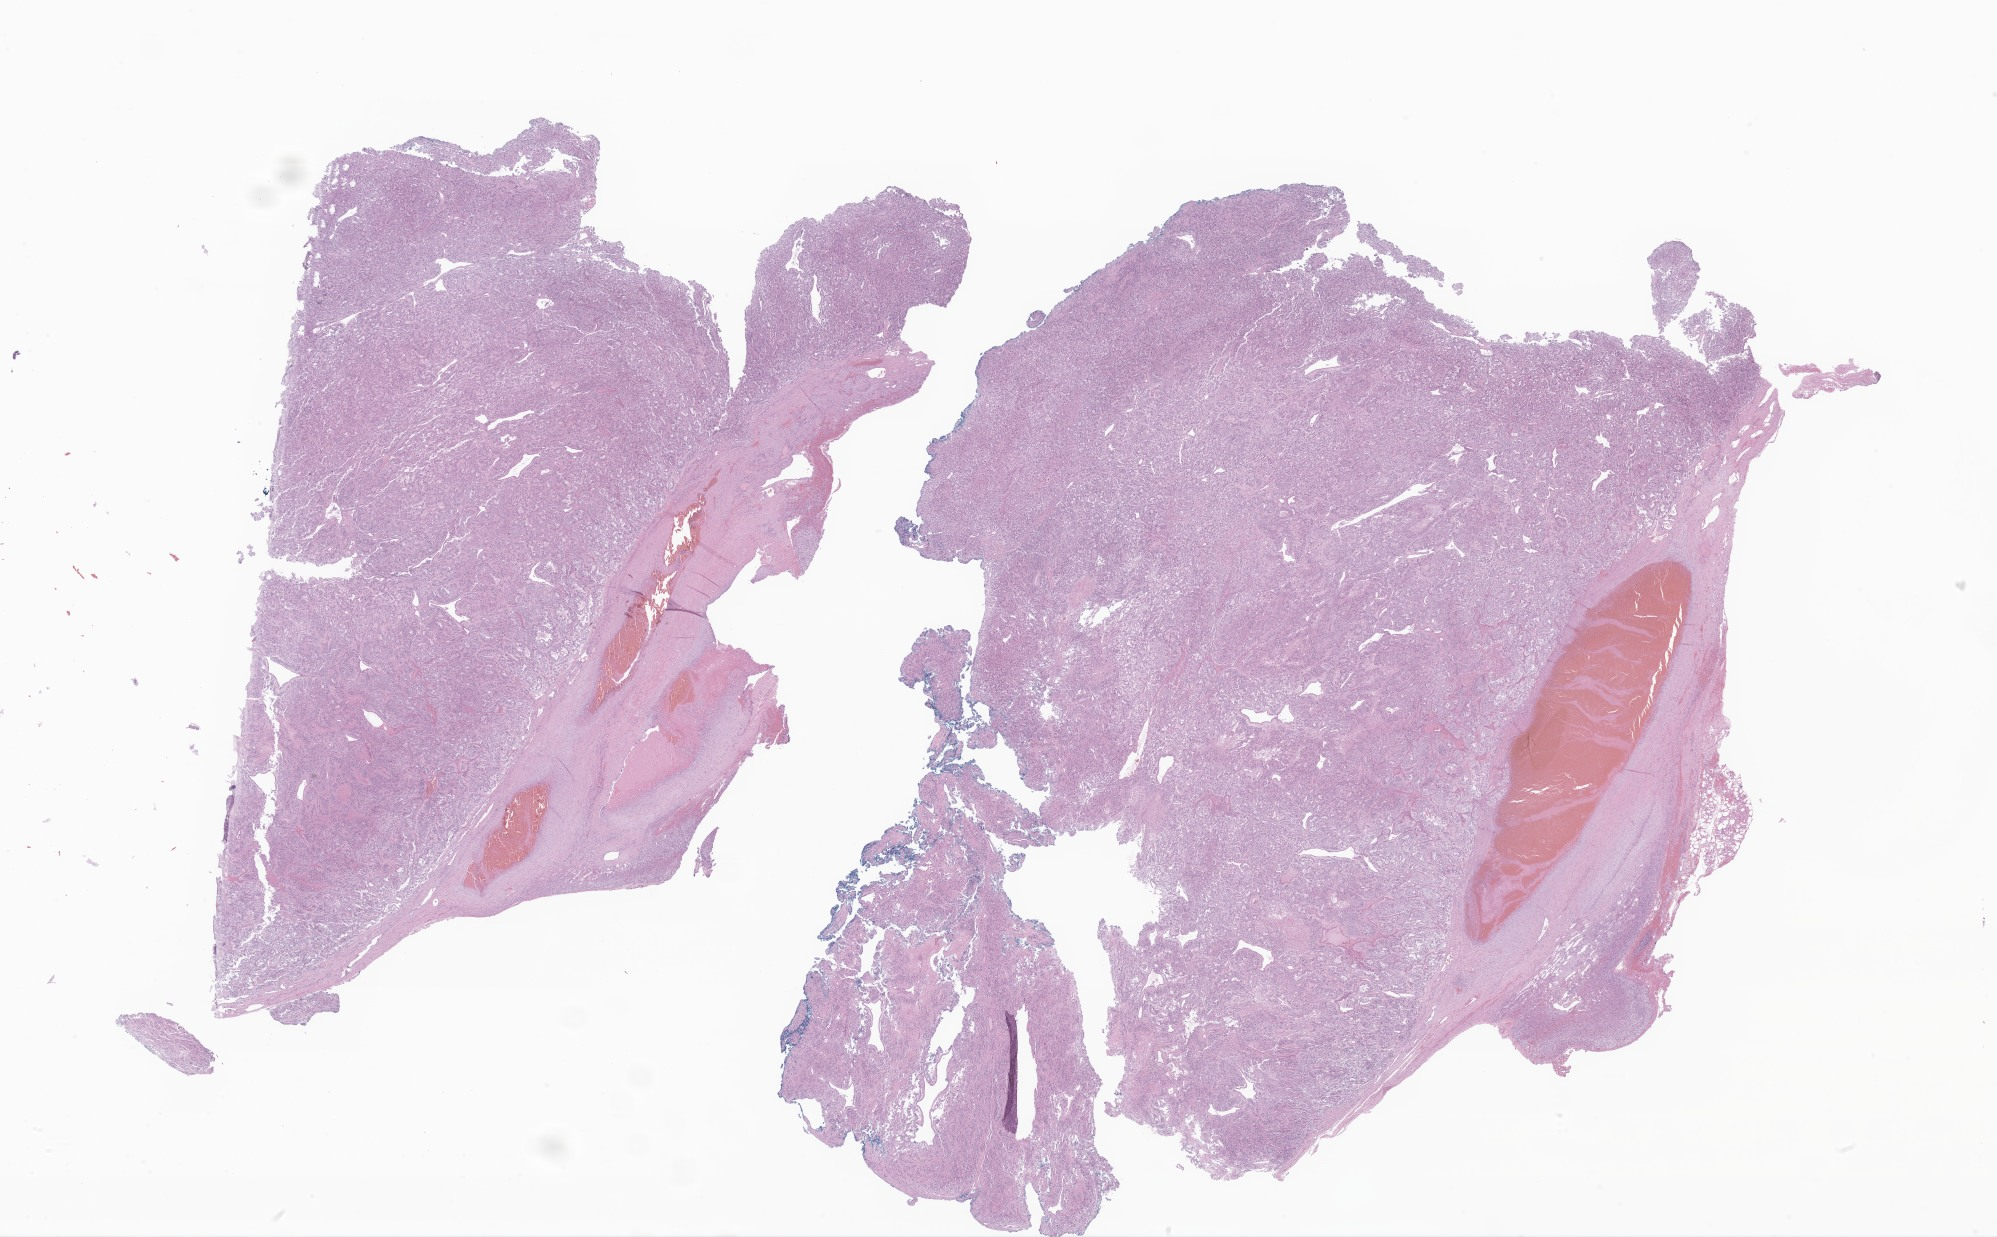
H&E whole-slide image of tumor tissue from the adrenal gland, low-resolution overview of the scanned area, about 33.7 x 20.9 mm; FFPE section. Patient male; age 85 months (7 years 1 month).
Diagnosis (ICD-O-3 morphology term): Pheochromocytoma, NOS.